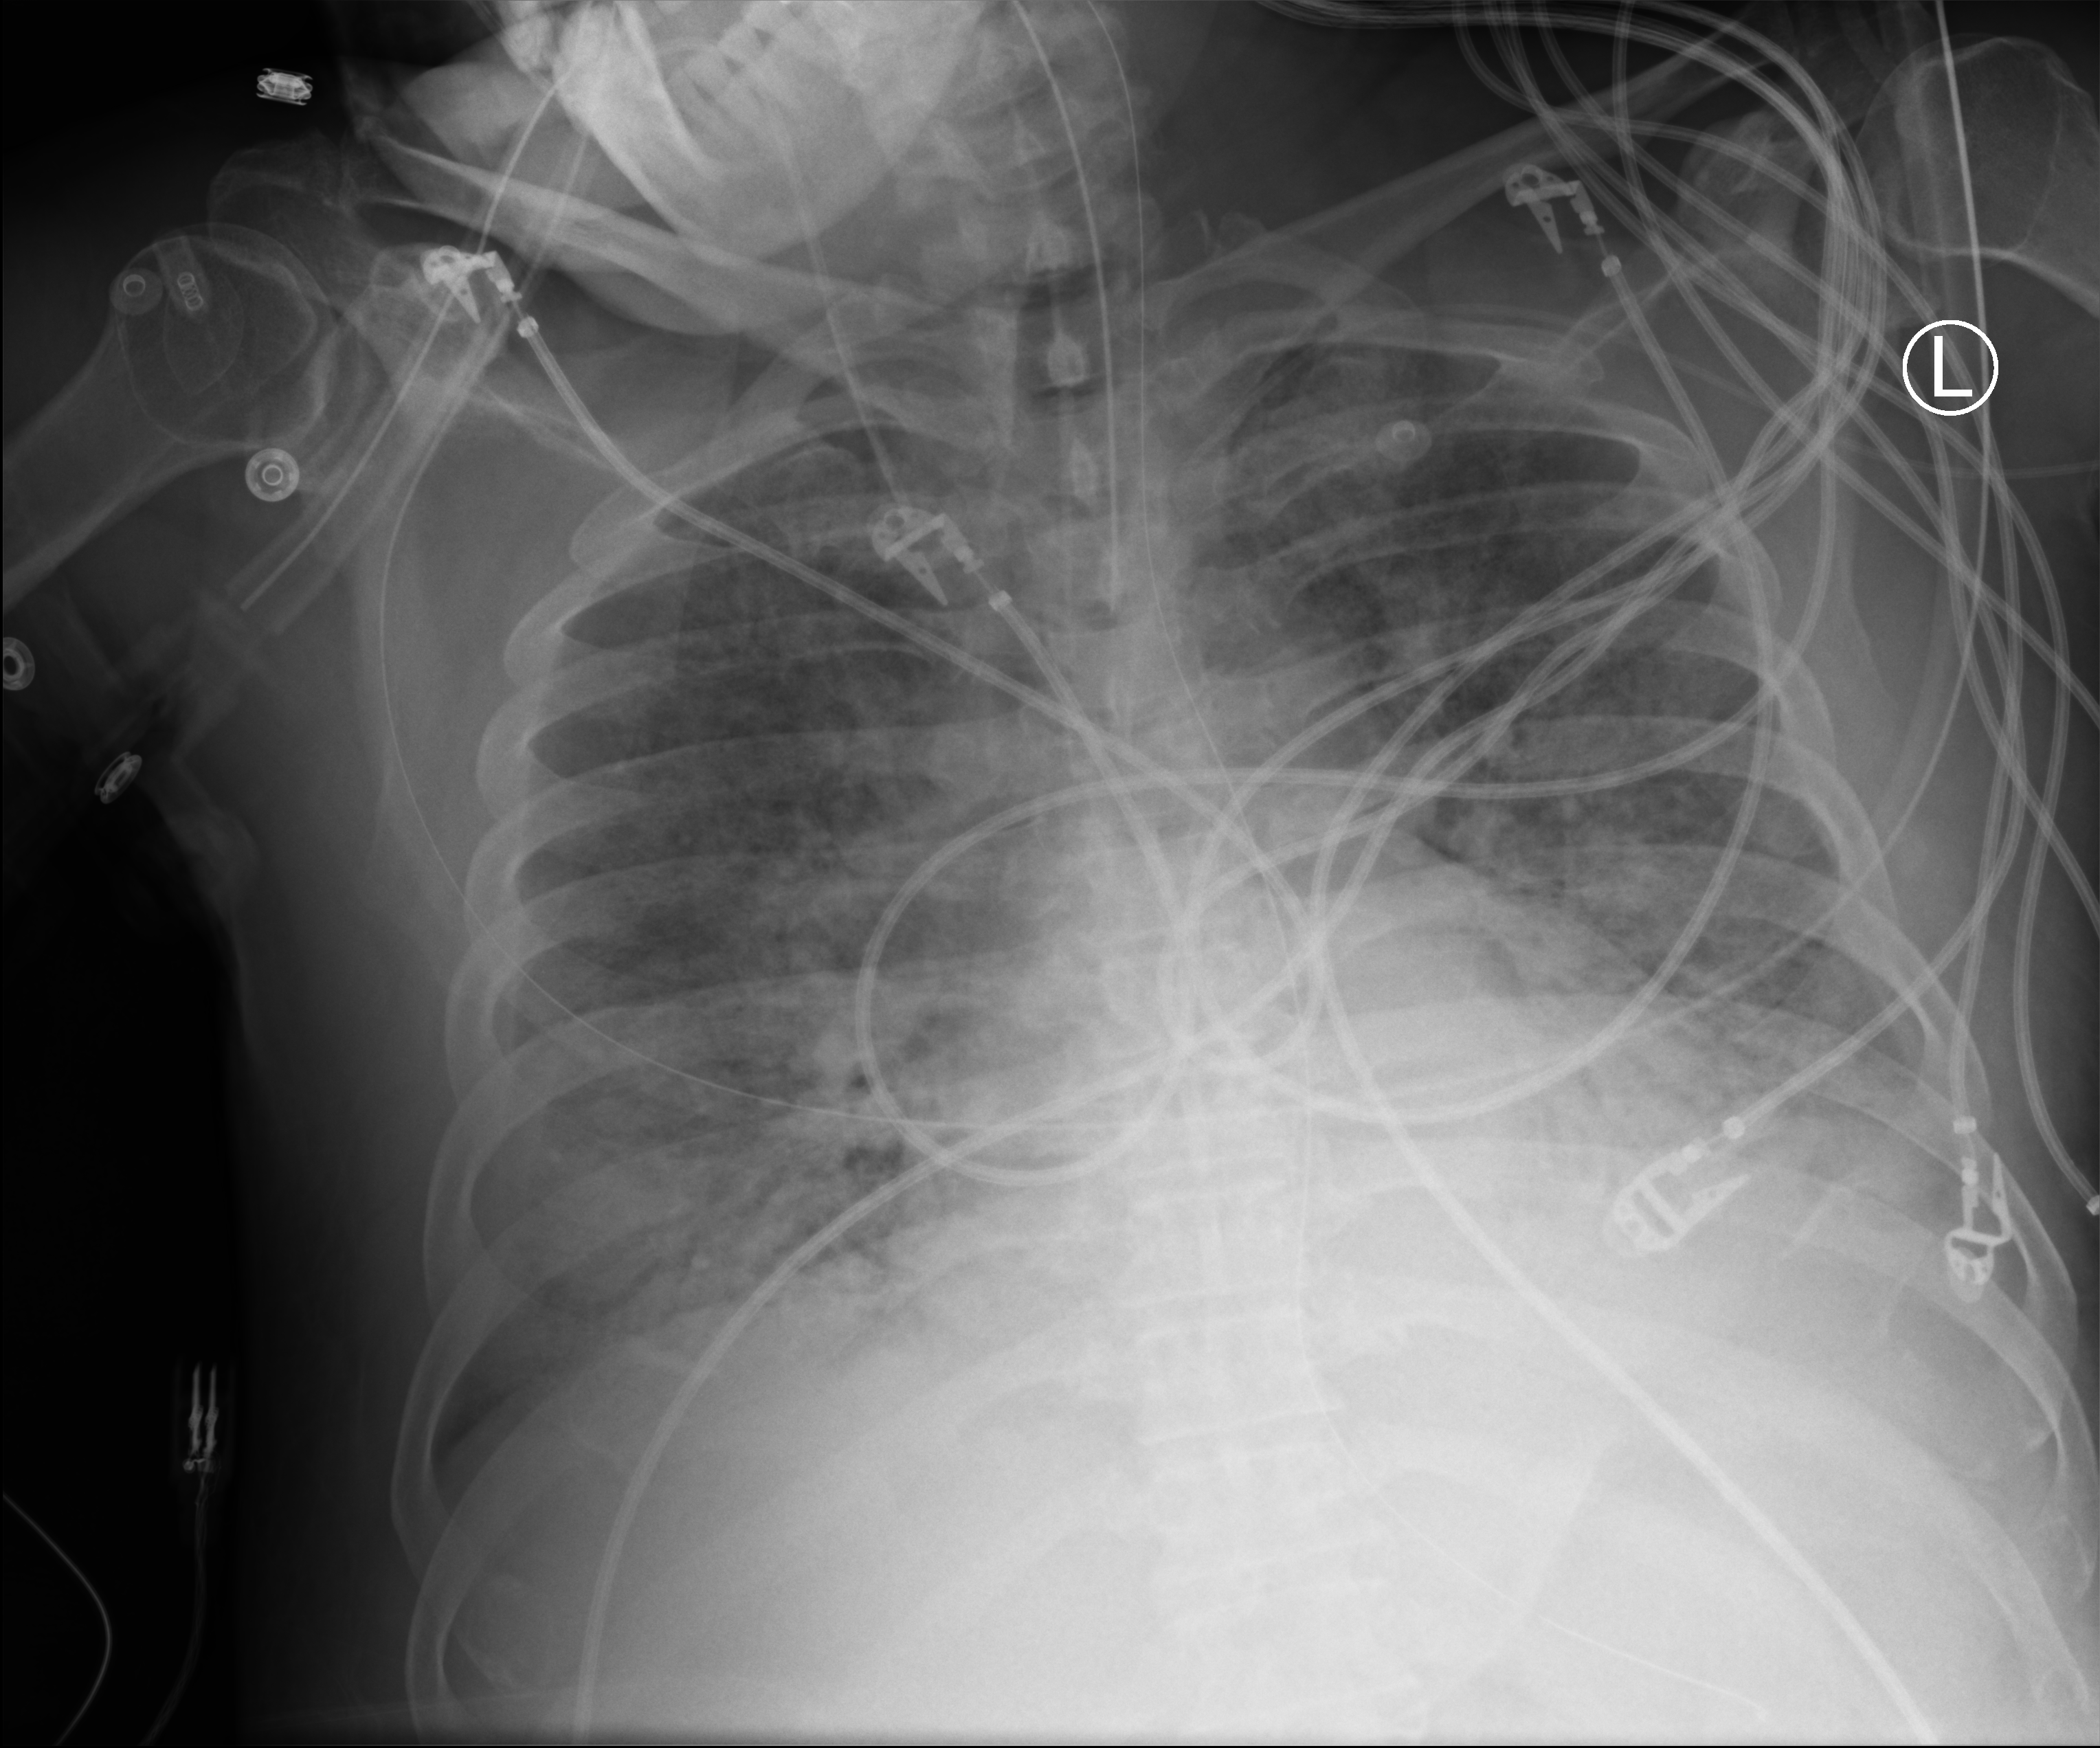
Chest X-ray (portable); anteroposterior (AP) projection. Patient hospitalised with COVID-19; male, aged 60–74 years.
From the hospital-stay record, not from the radiograph (when in the stay this image was taken is not recorded): admitted to intensive care during this hospital stay: yes; length of hospital stay: 28 days.